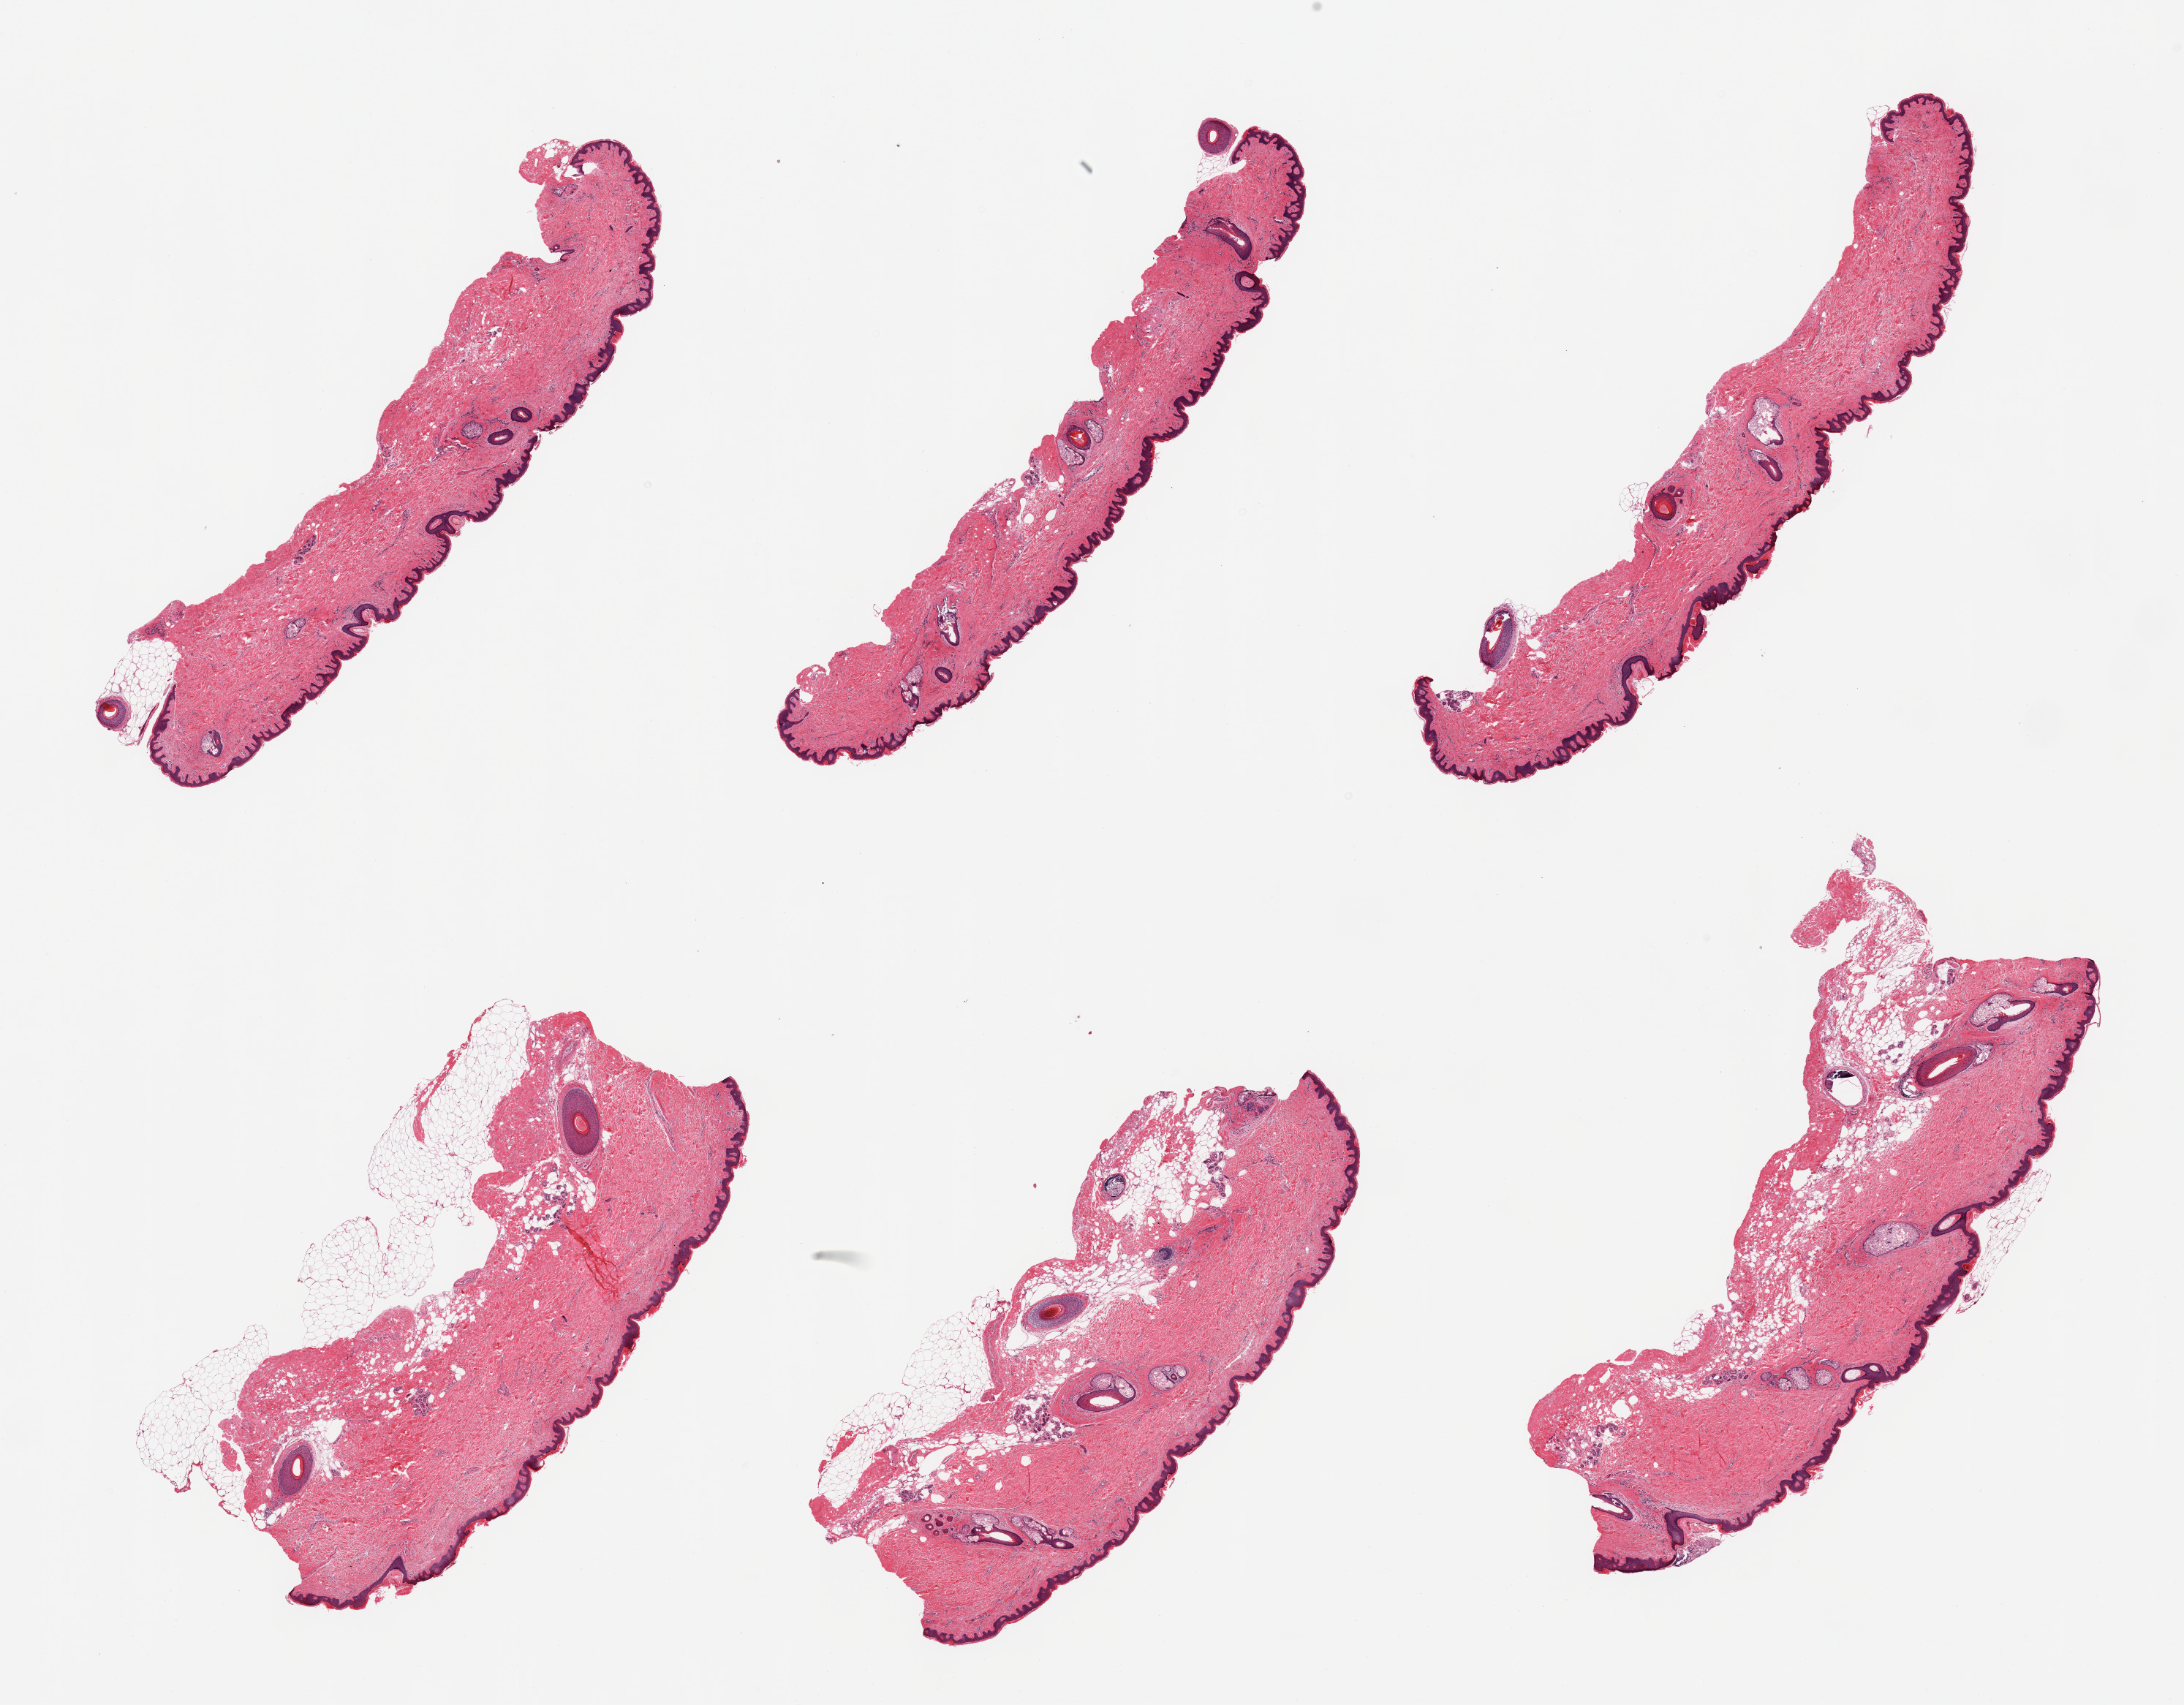
Haematoxylin and eosin whole-slide image, brightfield, shown as a low-resolution overview of the whole scanned area (about 23.6 x 18.4 mm), PAXgene-fixed, paraffin-embedded tissue, section of skin of suprapubic region (target tissue), tissue donor sample.
* reviewer comment on this tissue sample: 6 pieces; 1 with 1mm subcutaneous fat; 2 with 20% dermal fat